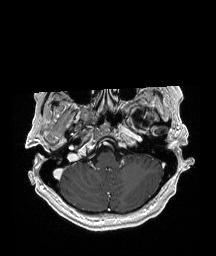
Brain MRI from a brain-tumour surgery series, one axial slice. Position 151 of 192 along the scan axis. T1-weighted post-contrast. 1 mm slice thickness. 216 × 256 image matrix. Case-level facts recorded for this patient, not image findings: histopathology: Glioblastoma; WHO grade: 4; IDH mutation: no; tumour location: Left Temporal.
Outlined on this slice (outlined manually by an expert reader):
- previous resection cavity: bounding box [x1, y1, x2, y2] px = [129, 109, 152, 131]